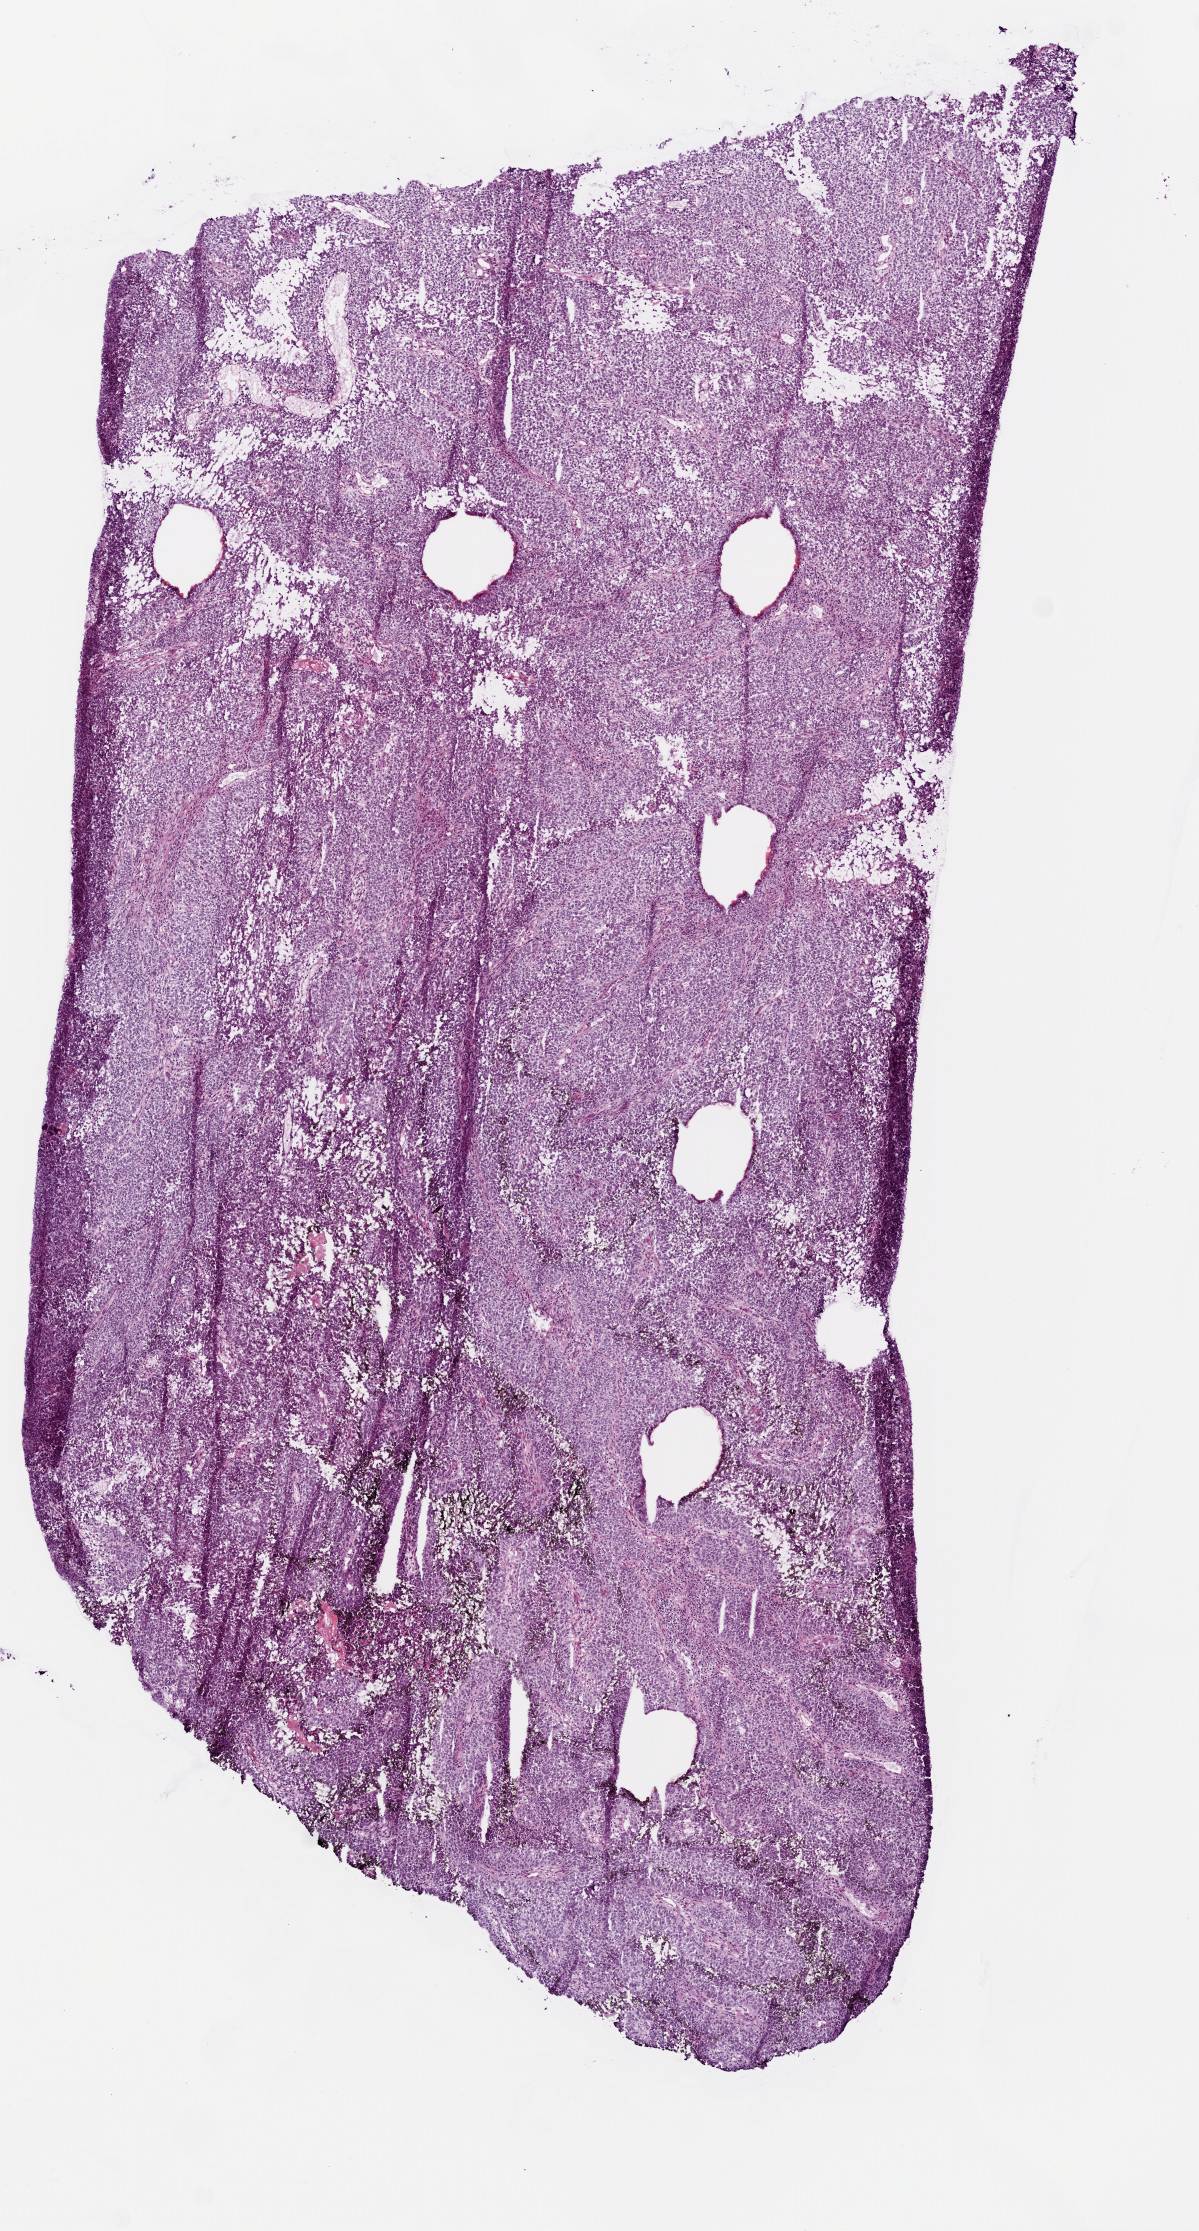
H&E whole-slide image — whole scanned area (about 4.8 x 9.0 mm) shown as a low-resolution overview; frozen section from the top of the tissue portion; sample: primary tumour, uterus. Patient: female, age at initial diagnosis 47 years. Histologic grade: G3 (poorly differentiated). Pathologist review of this section (percent, as recorded): tumour cells 90%, tumour nuclei 85%, normal cells 0%, stromal cells 10%, necrosis 0%. Infiltration values recorded for this section: lymphocyte infiltration 0%, monocyte infiltration 0%, neutrophil infiltration 0%.
Lymph nodes positive (case pathology): 0 of 15 examined. FIGO stage: IA. Diagnosis: Endometrioid adenocarcinoma, NOS.